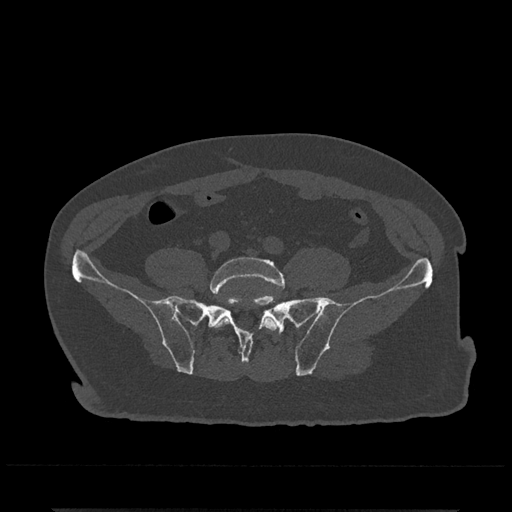
CT including the spine, one axial slice. Slice 52 of 797 in the series (ordered by position). 120 kVp. Bone window (W 1800 / L 400 HU). 512 × 512 image matrix, field of view 393 × 393 mm. Patient: male, 67 years. From the clinical record (not read from this slice): primary cancer: prostate.
Structures marked on this image (semi-automatically segmented with operator editing):
- L5 vertebra: bounding box (x1, y1, x2, y2) in pixels: (210, 257, 284, 332)